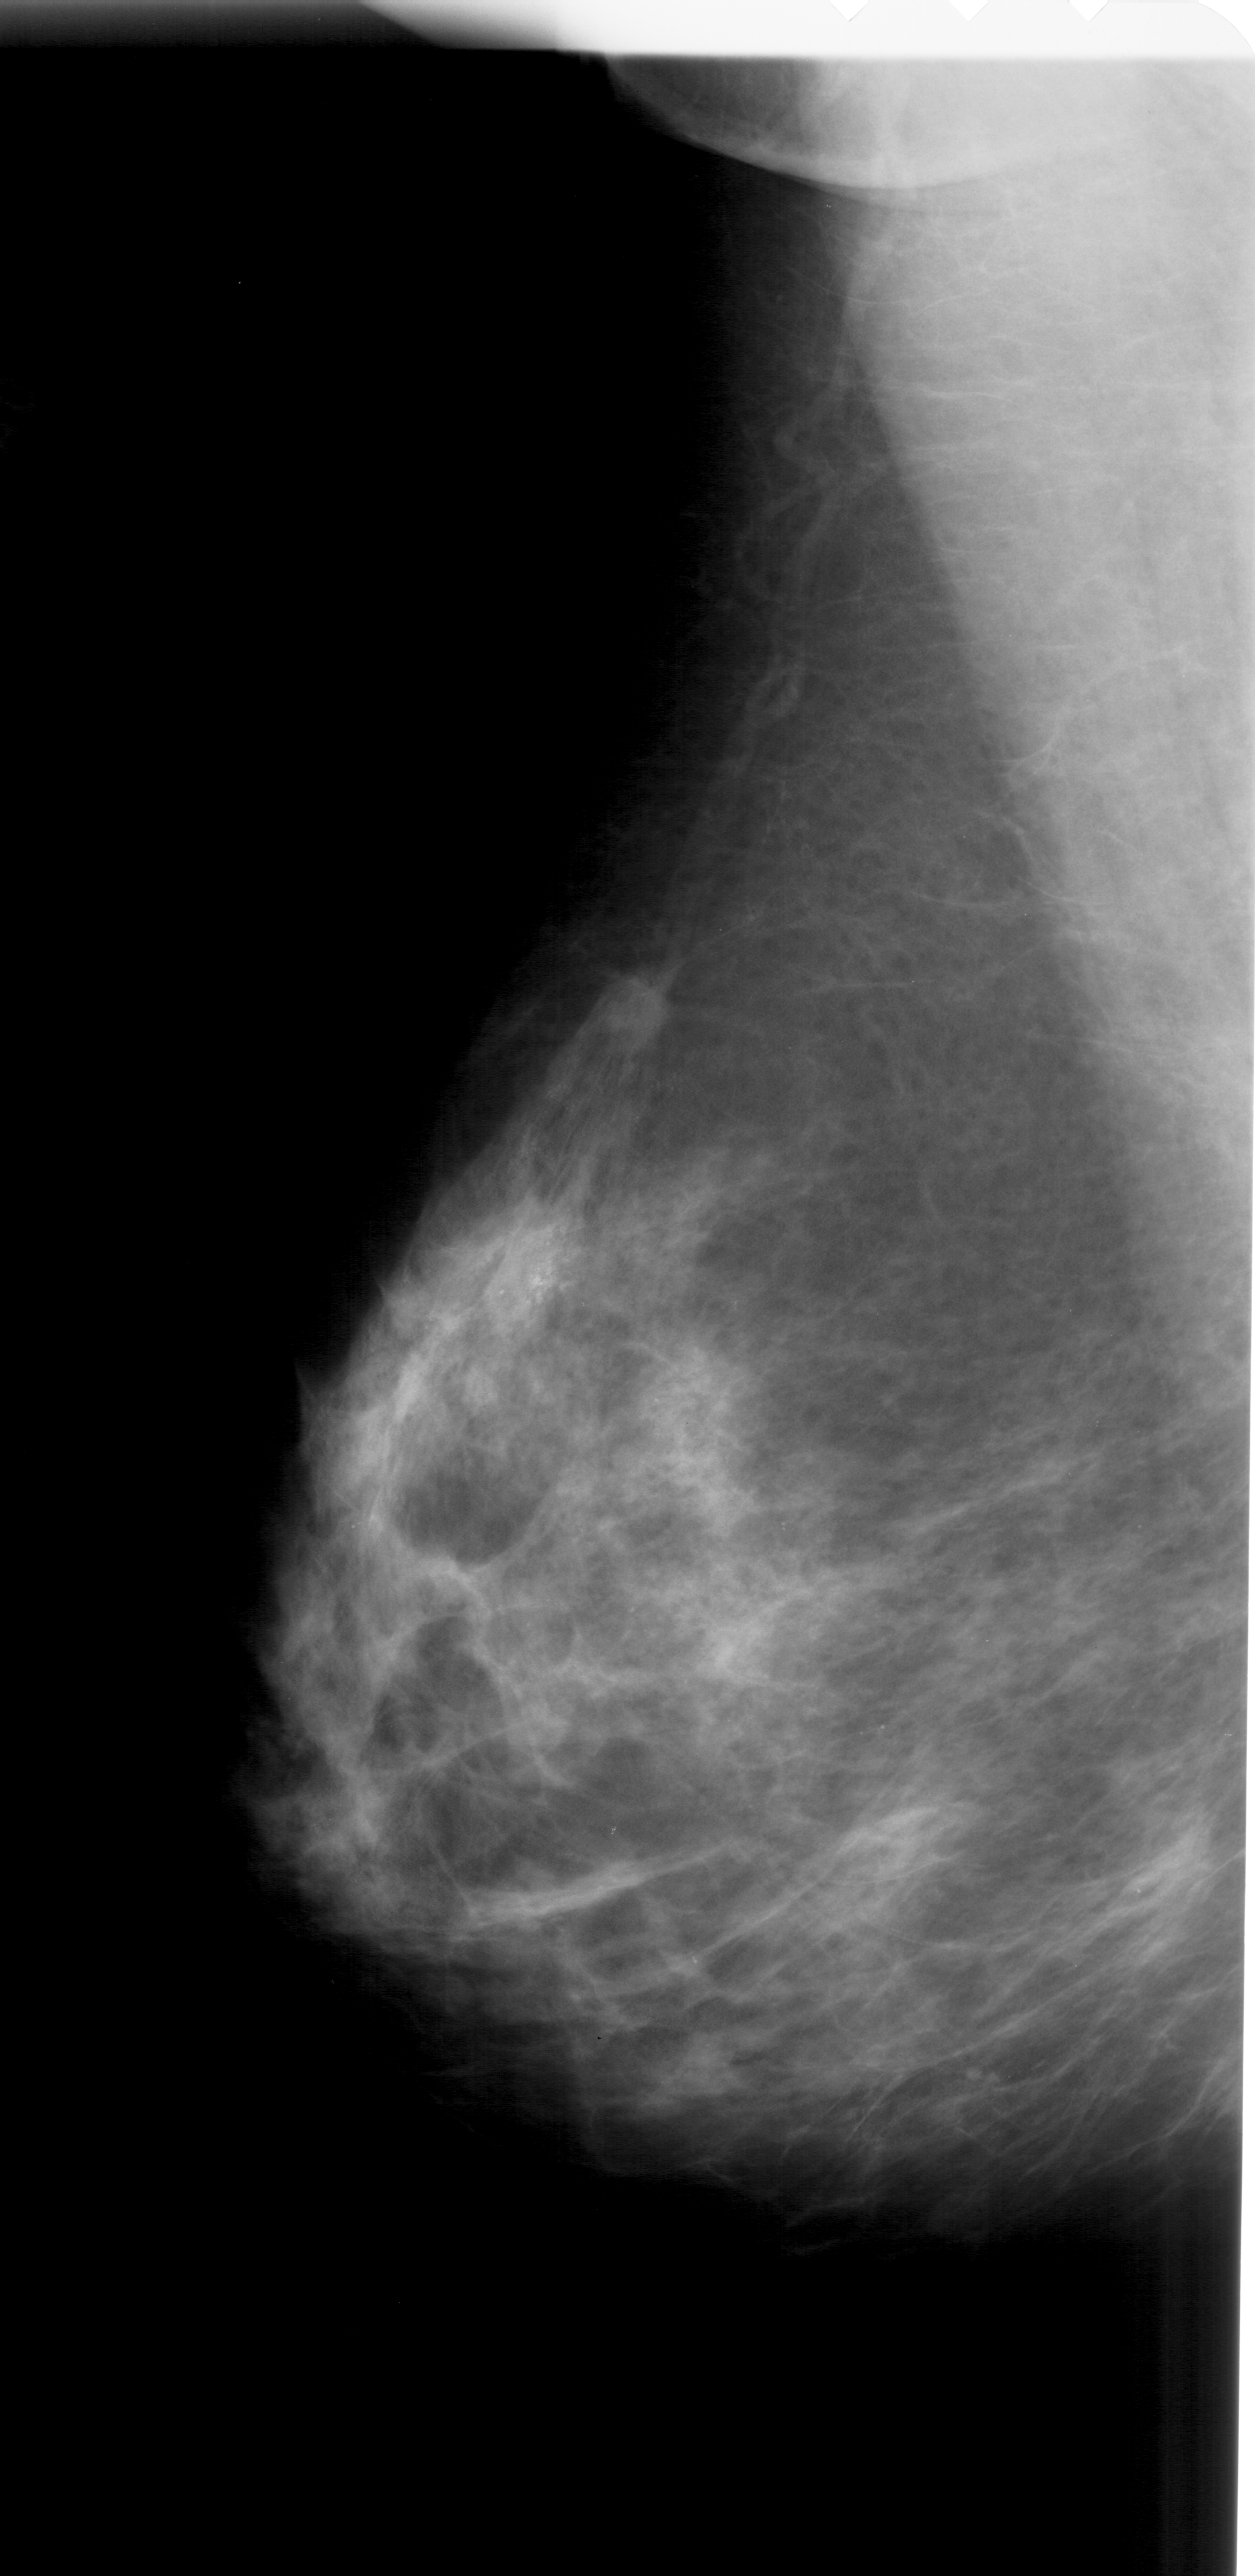
Scanned film-screen mammogram; left breast; mediolateral oblique (MLO) view.
- Marked findings (only marked abnormalities are described; nothing is implied about the rest of the image): calcifications, morphology pleomorphic, distribution clustered; BI-RADS assessment category 4; pathology (as recorded): malignant.